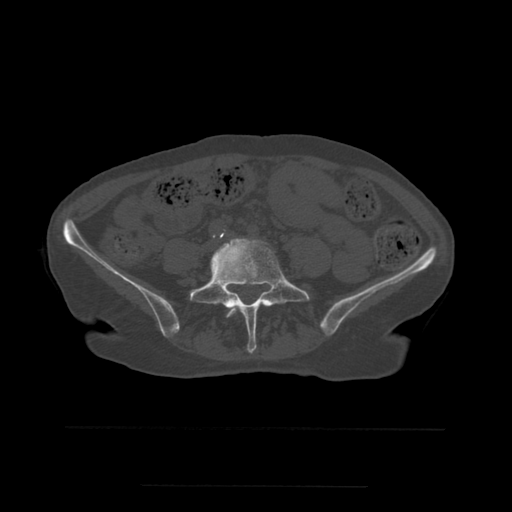
CT including the spine, one axial slice. Position 149 of 544 along the scan axis. Bone window (W 1800 / L 400 HU). 1.25 mm slice thickness. 512 × 512 image matrix, field of view 350 × 350 mm. Patient age 58 years. From the clinical record (not read from this slice): primary cancer: lung.
Outlined on this slice (semi-automatically segmented with operator editing):
- L4 vertebra: box from (x=226, y=306) to (x=239, y=318) px
- L5 vertebra: (x=190, y=239)–(x=302, y=353)